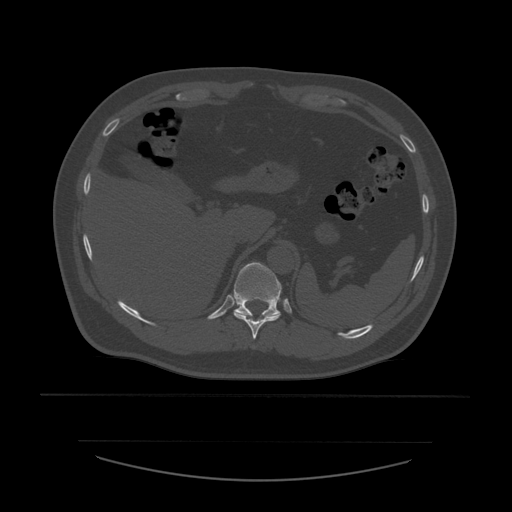
CT including the spine, one axial slice; reconstruction kernel STANDARD; 120 kVp; bone window (W 1800 / L 400 HU); 1.25 mm slice thickness; 512 × 512 image matrix, field of view 441 × 441 mm. Patient age 44 years. From the clinical record (not read from this slice): primary cancer: soft tissue sarcoma.
Structures marked on this image (semi-automatically segmented with operator editing):
- T10 vertebra: bounding box <234,313,281,340> (left, top, right, bottom; pixels)
- T11 vertebra: <234,262,283,317>